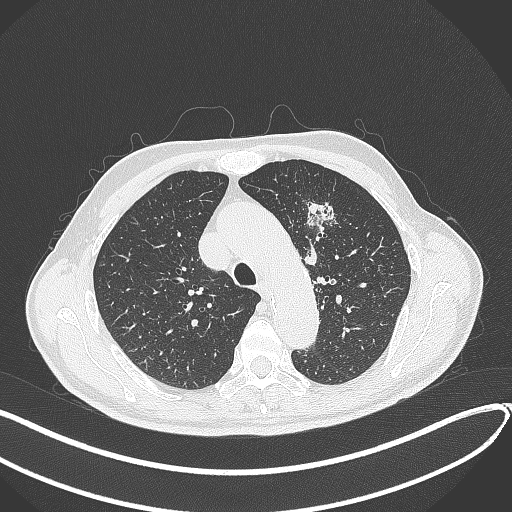
Chest CT, one axial slice; position 304 of 459 along the scan axis; reconstruction kernel B70f; lung window (W 1500 / L -600 HU); 1 mm slice thickness; 512 × 512 image matrix. Male patient, age 74 years. Case-level facts recorded for this patient, not image findings: clinical TNM (as recorded): T2b N0 M1c.
Annotated regions visible in this slice (bounding box drawn by a radiologist):
- lung tumour (recorded histology: adenocarcinoma): bounding box [x1, y1, x2, y2] px = [304, 196, 342, 245]